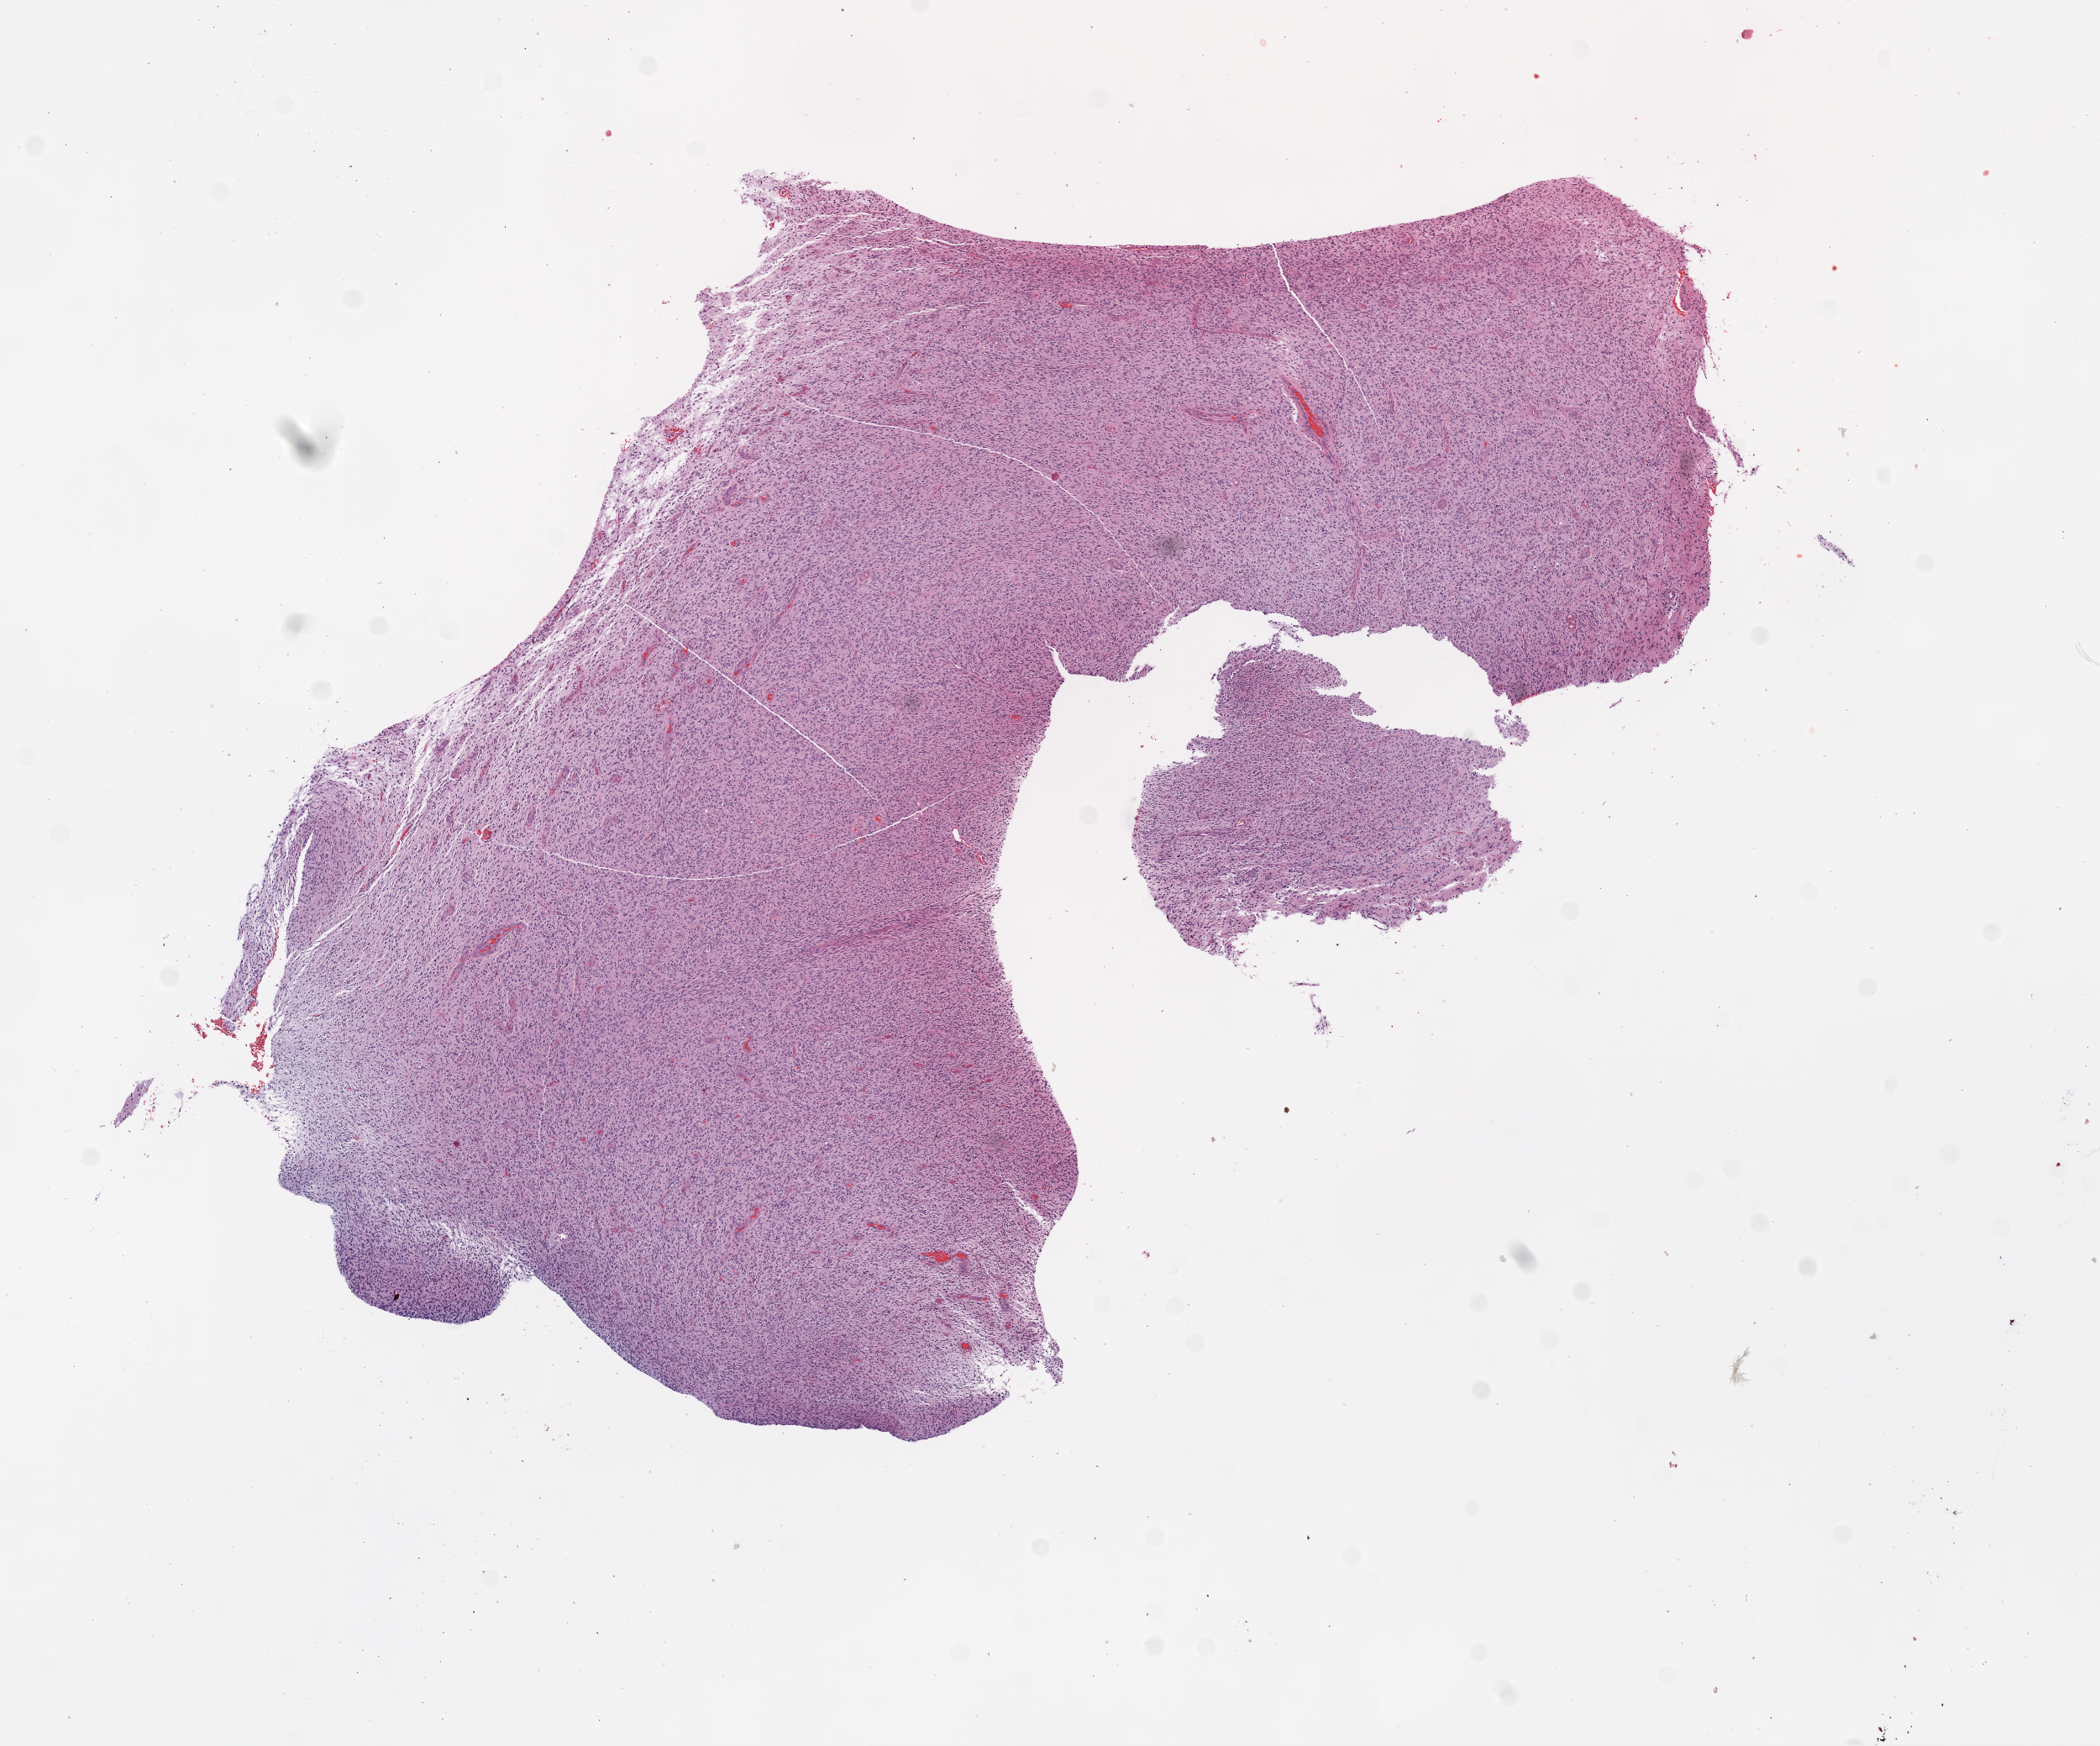
Whole-slide histology image, H&E, a low-resolution overview of the entire scanned area, about 10.0 x 8.3 mm (slide scanned at 20x). FFPE section. Sample: primary tumour, brain. Patient: female, age at initial diagnosis 84 years.
Diagnosis: Glioblastoma.